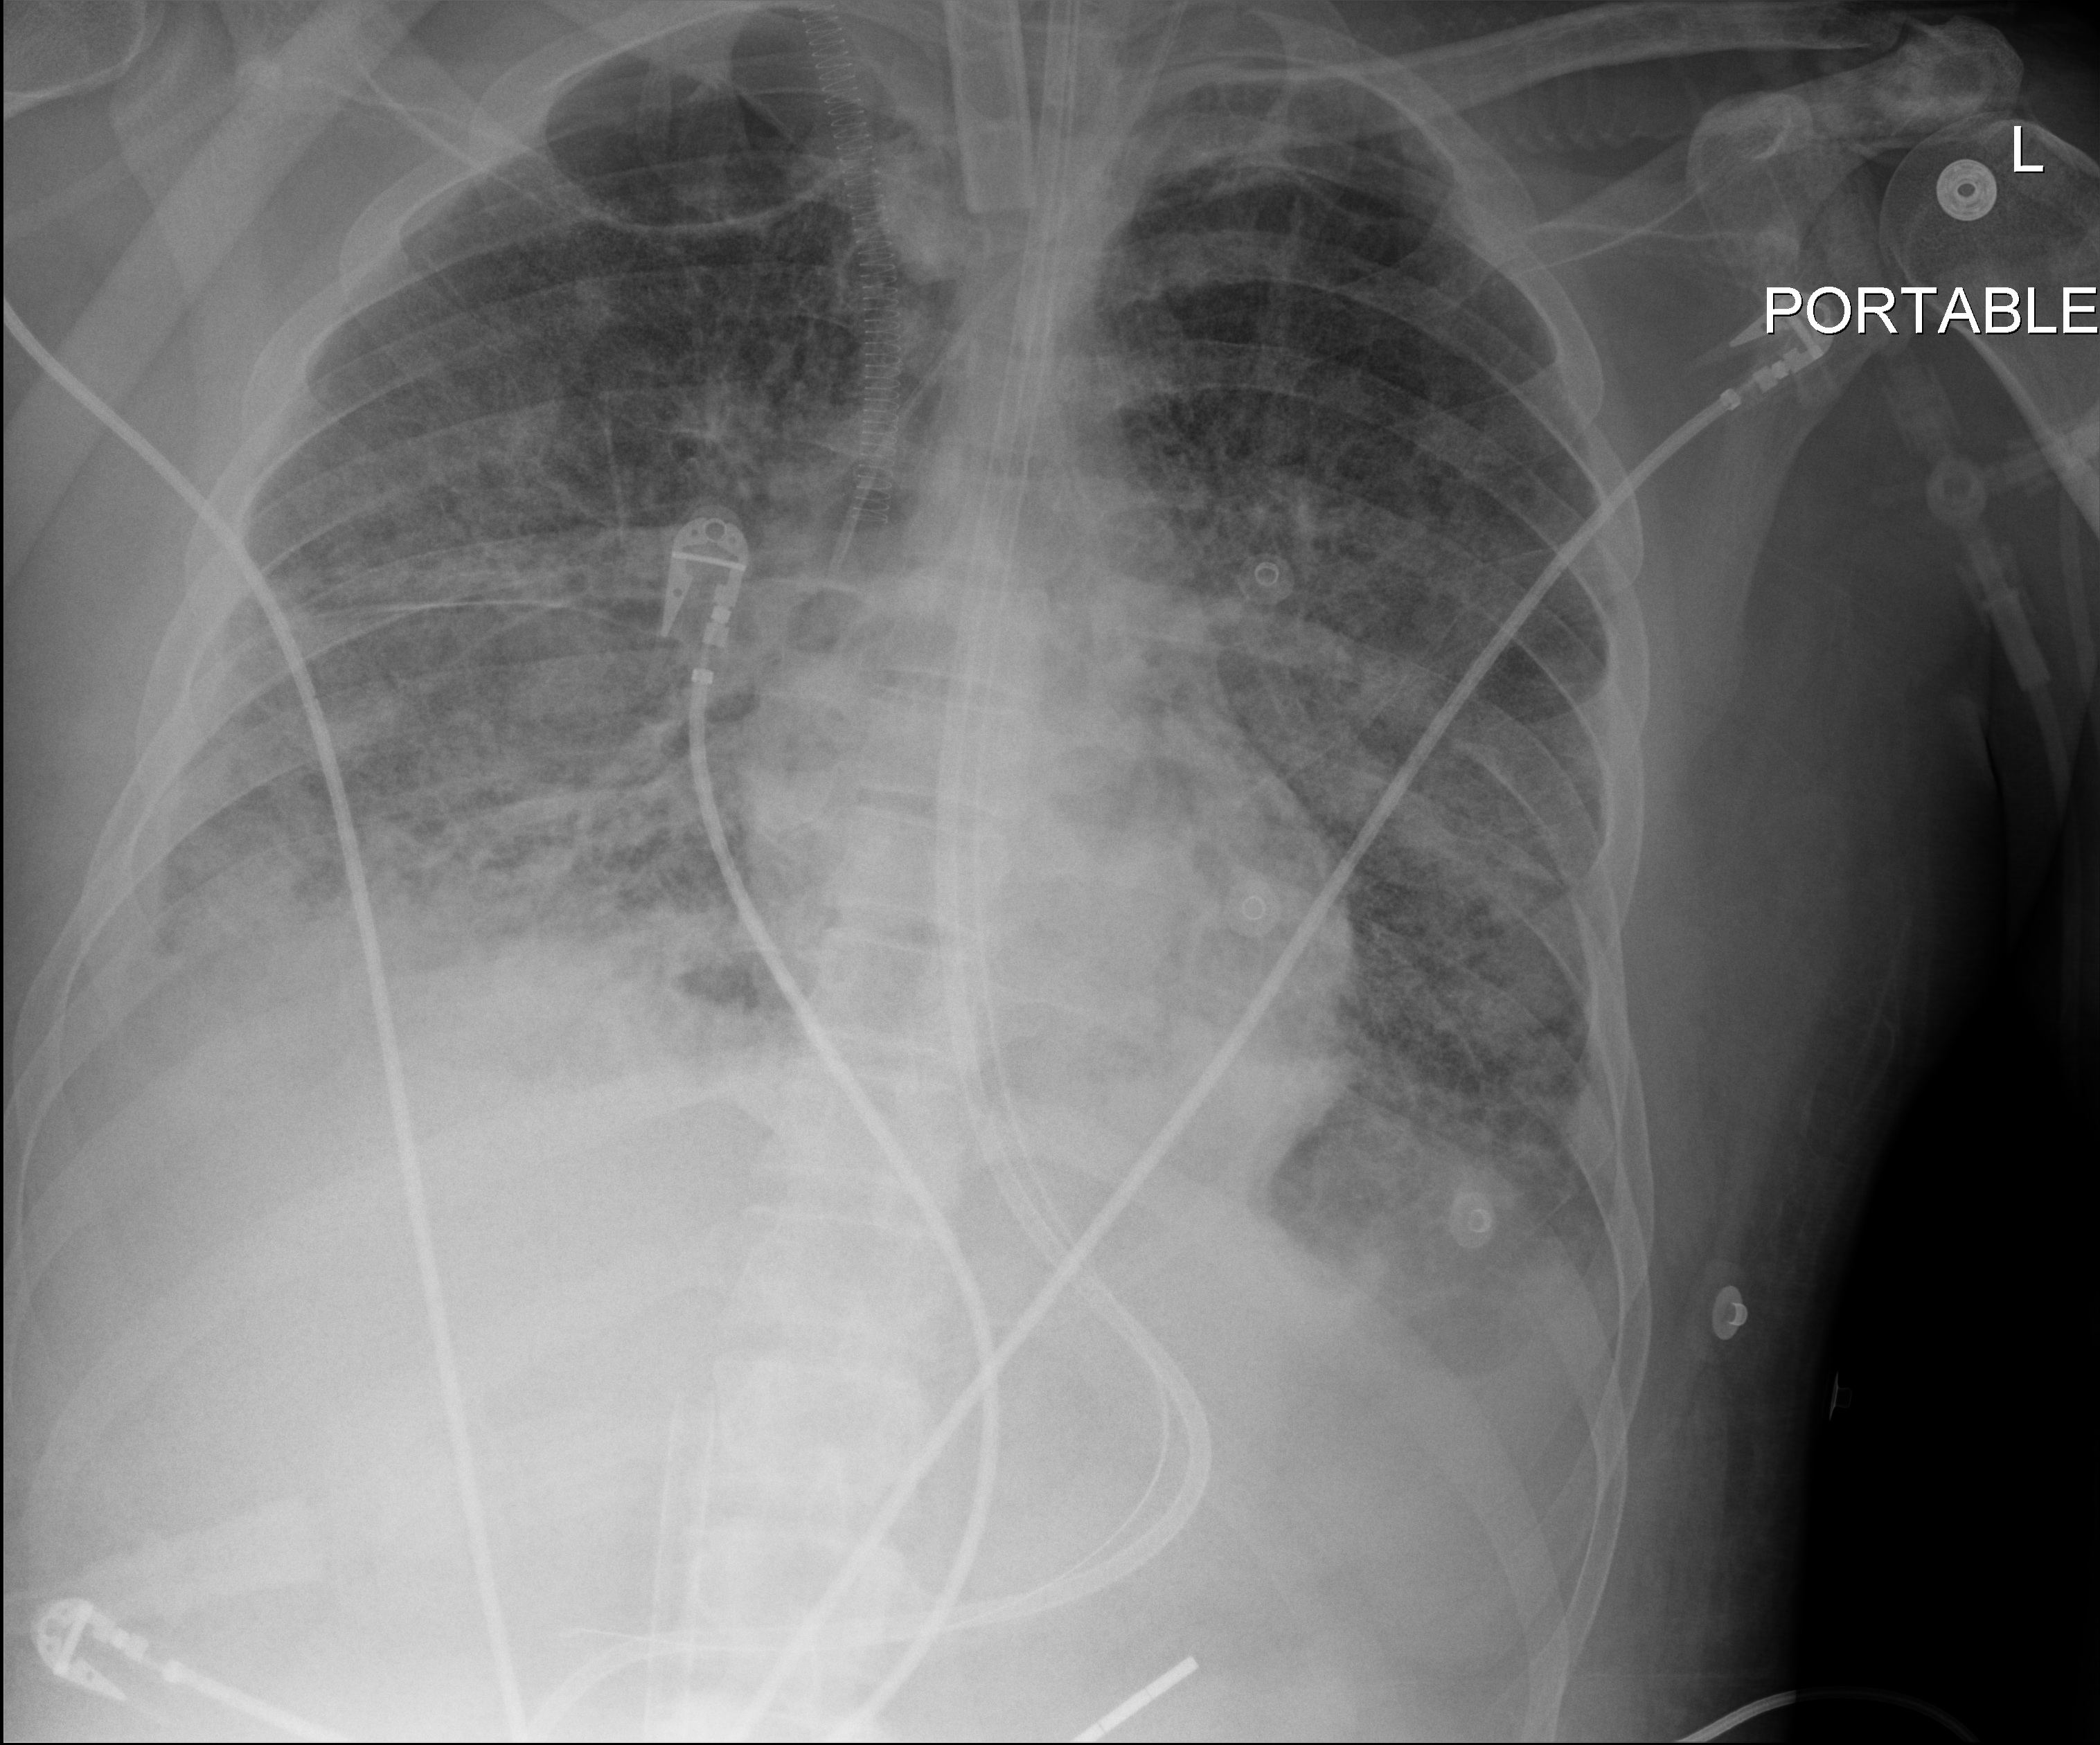
Portable chest radiograph; anteroposterior (AP) projection. Adult patient hospitalised with COVID-19, age 18–59 years.
Admission-level facts for this patient (not findings on this image; timing relative to this image not recorded):
- hypertension (admission record): no
- mechanically ventilated during this hospital stay: yes